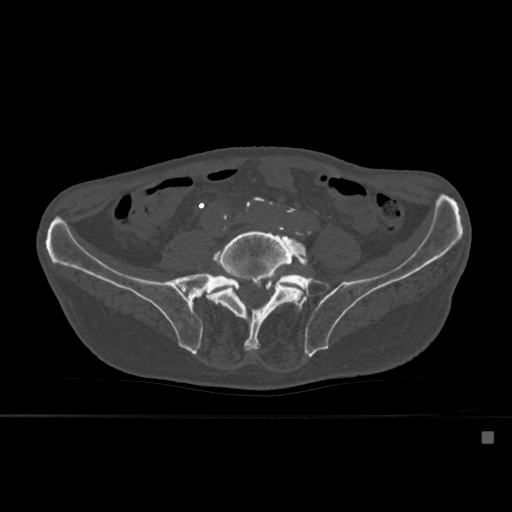
CT including the spine, one axial slice. Position 173 of 527 along the scan axis. Bone window (W 1800 / L 400 HU). 512 × 512 image matrix, field of view 373 × 373 mm. Male patient, age 78 years. Case-level facts recorded for this patient, not image findings: primary cancer: prostate.
Outlined on this slice (semi-automatic segmentation, software-assisted and operator-edited):
- L4 vertebra: bounding box [x1, y1, x2, y2] px = [281, 302, 283, 304]
- L5 vertebra: [206, 227, 308, 351]